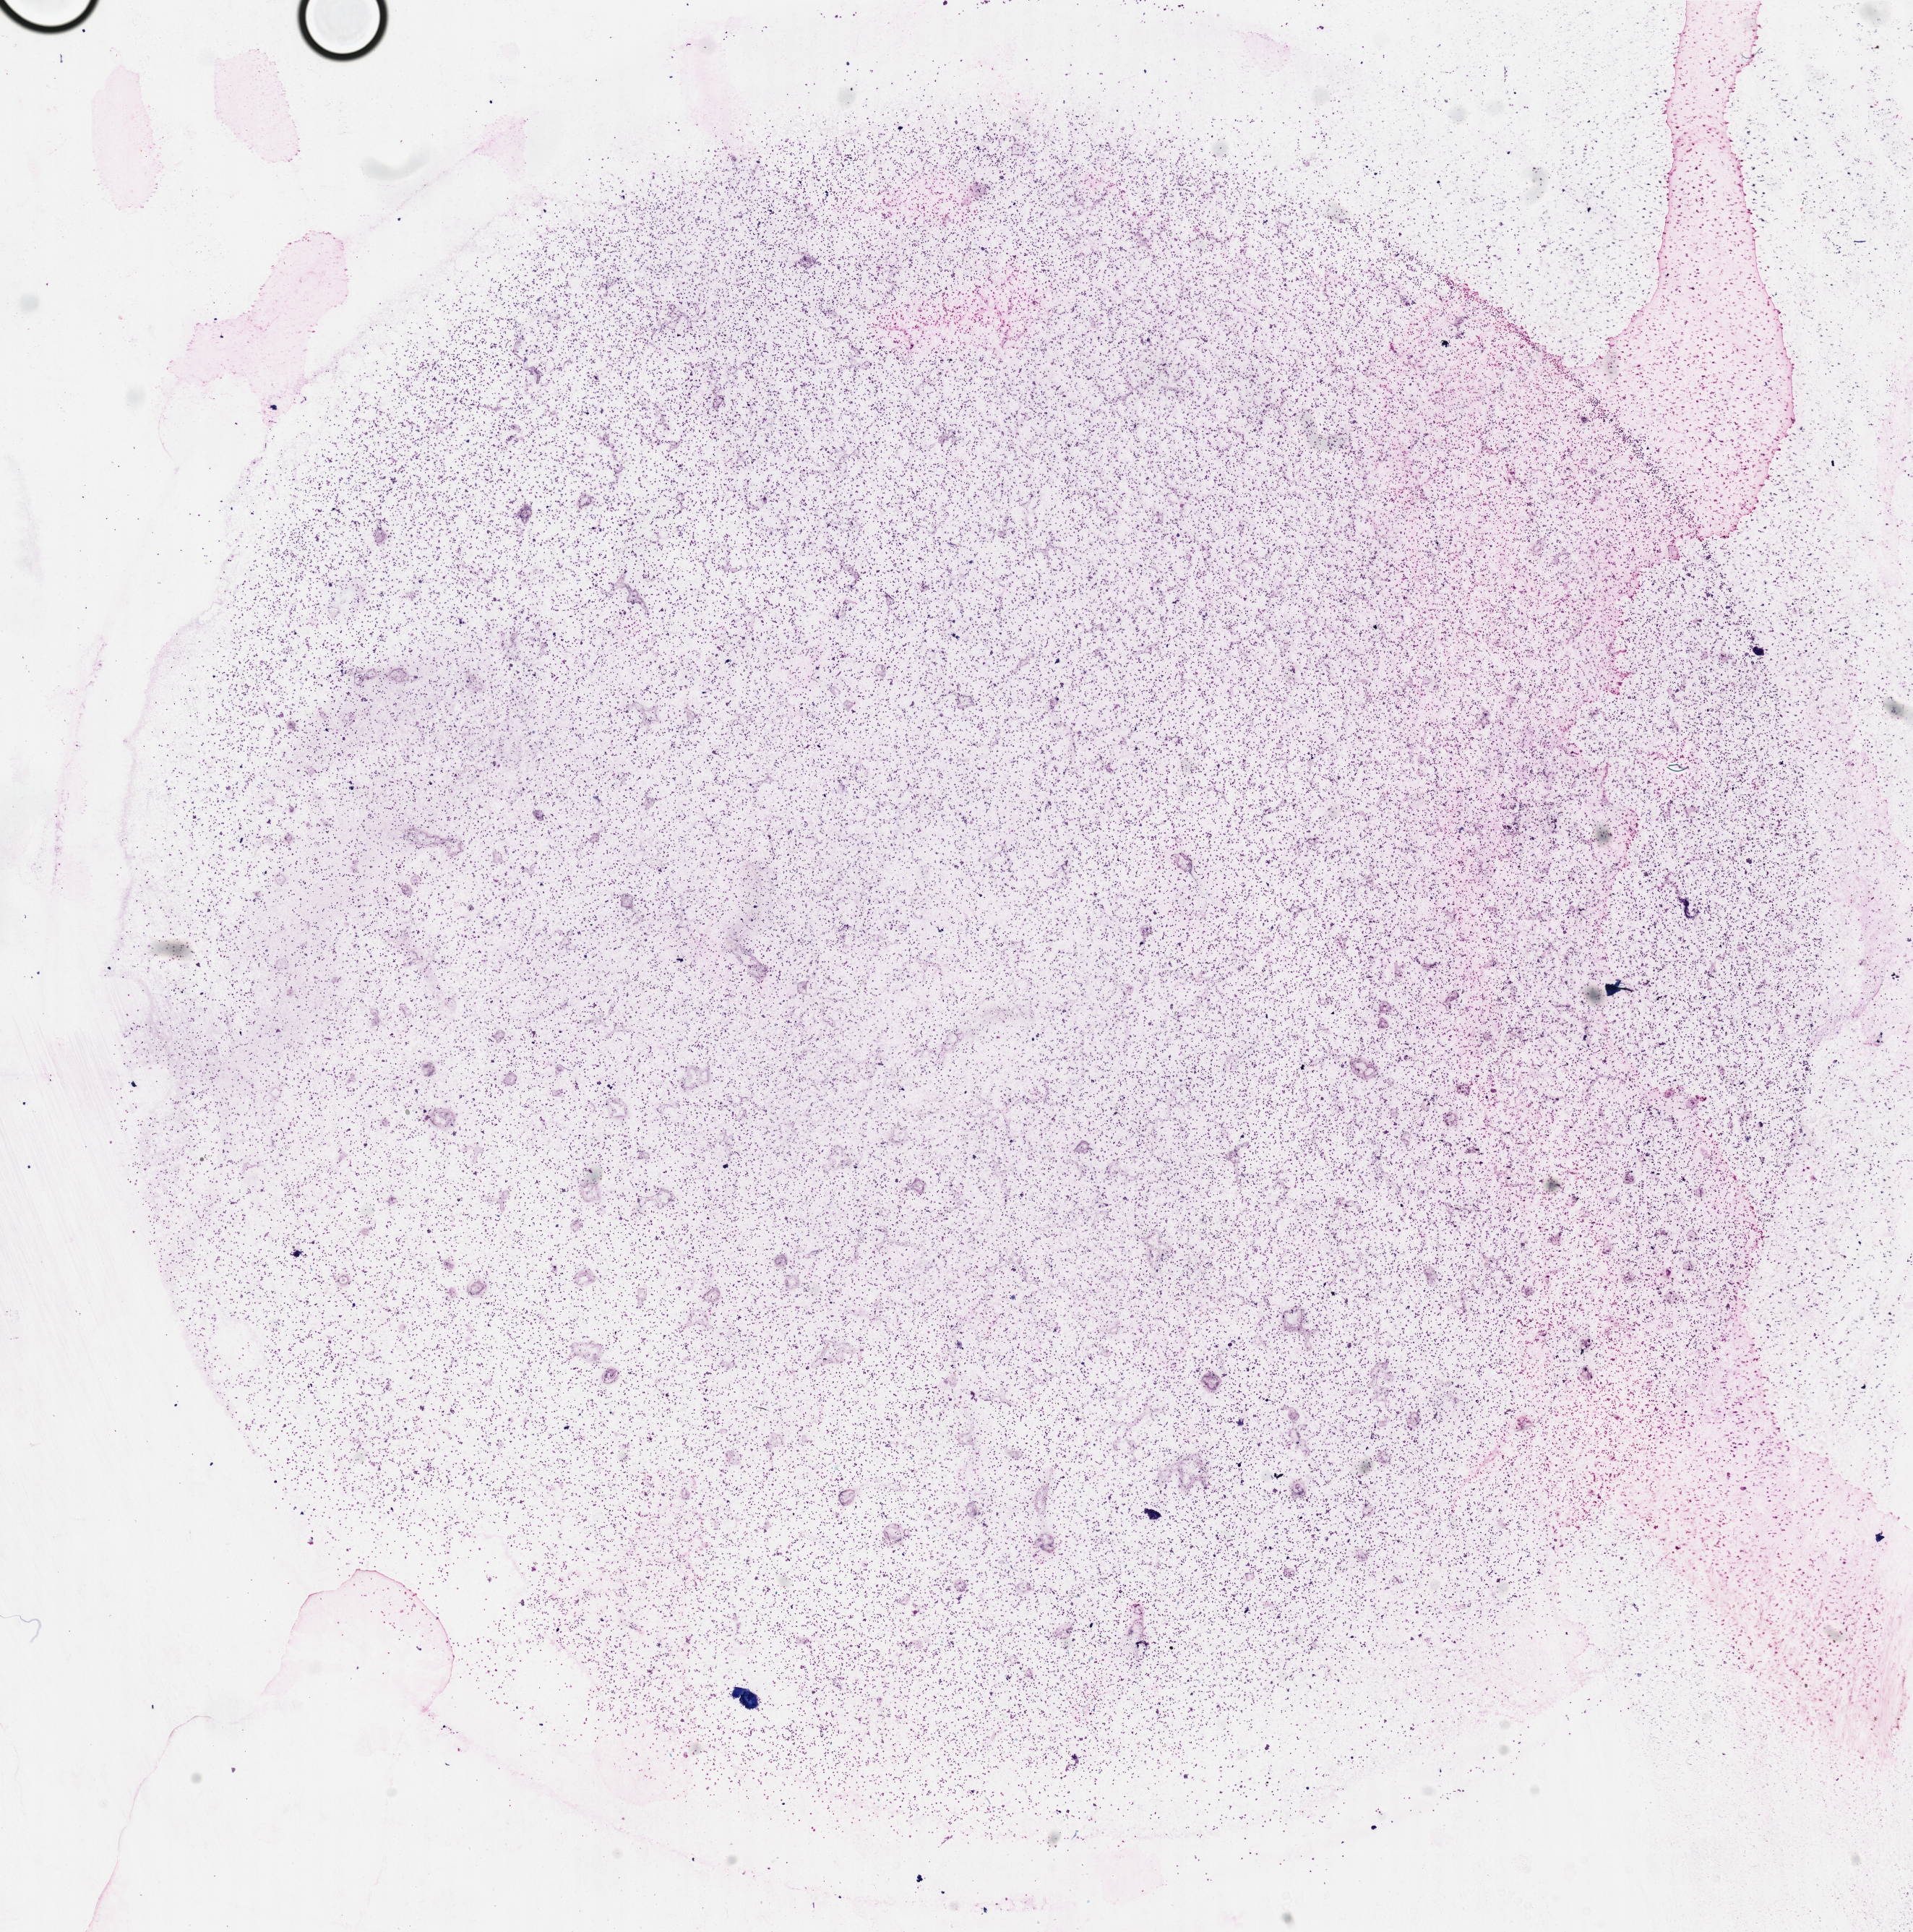
Whole-slide histology image, Hematoxylin and eosin (H&E) stained — low-resolution overview of the scanned area, about 20.9 x 21.1 mm (slide scanned at 40x); bone marrow (leukaemic) sample. Male, 58 y/o. Blasts: 95%.
• FAB classification: M0
• diagnosis: Acute Myeloid Leukemia
• WHO classification: AML with minimal differentiation